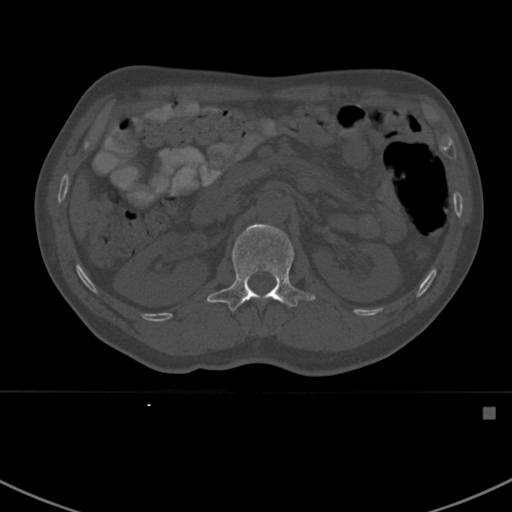
CT including the spine, one axial slice. Position 310 of 412 along the scan axis. Reconstruction kernel Br40s. Bone window (W 1800 / L 400 HU). 512 × 512 image matrix, field of view 358 × 358 mm. Male patient, age 59 years. From the clinical record (not read from this slice): primary cancer: prostate.
Annotated regions visible in this slice (semi-automatically segmented with operator editing):
- L1 vertebra: bounding box [x1, y1, x2, y2] px = [207, 224, 316, 312]